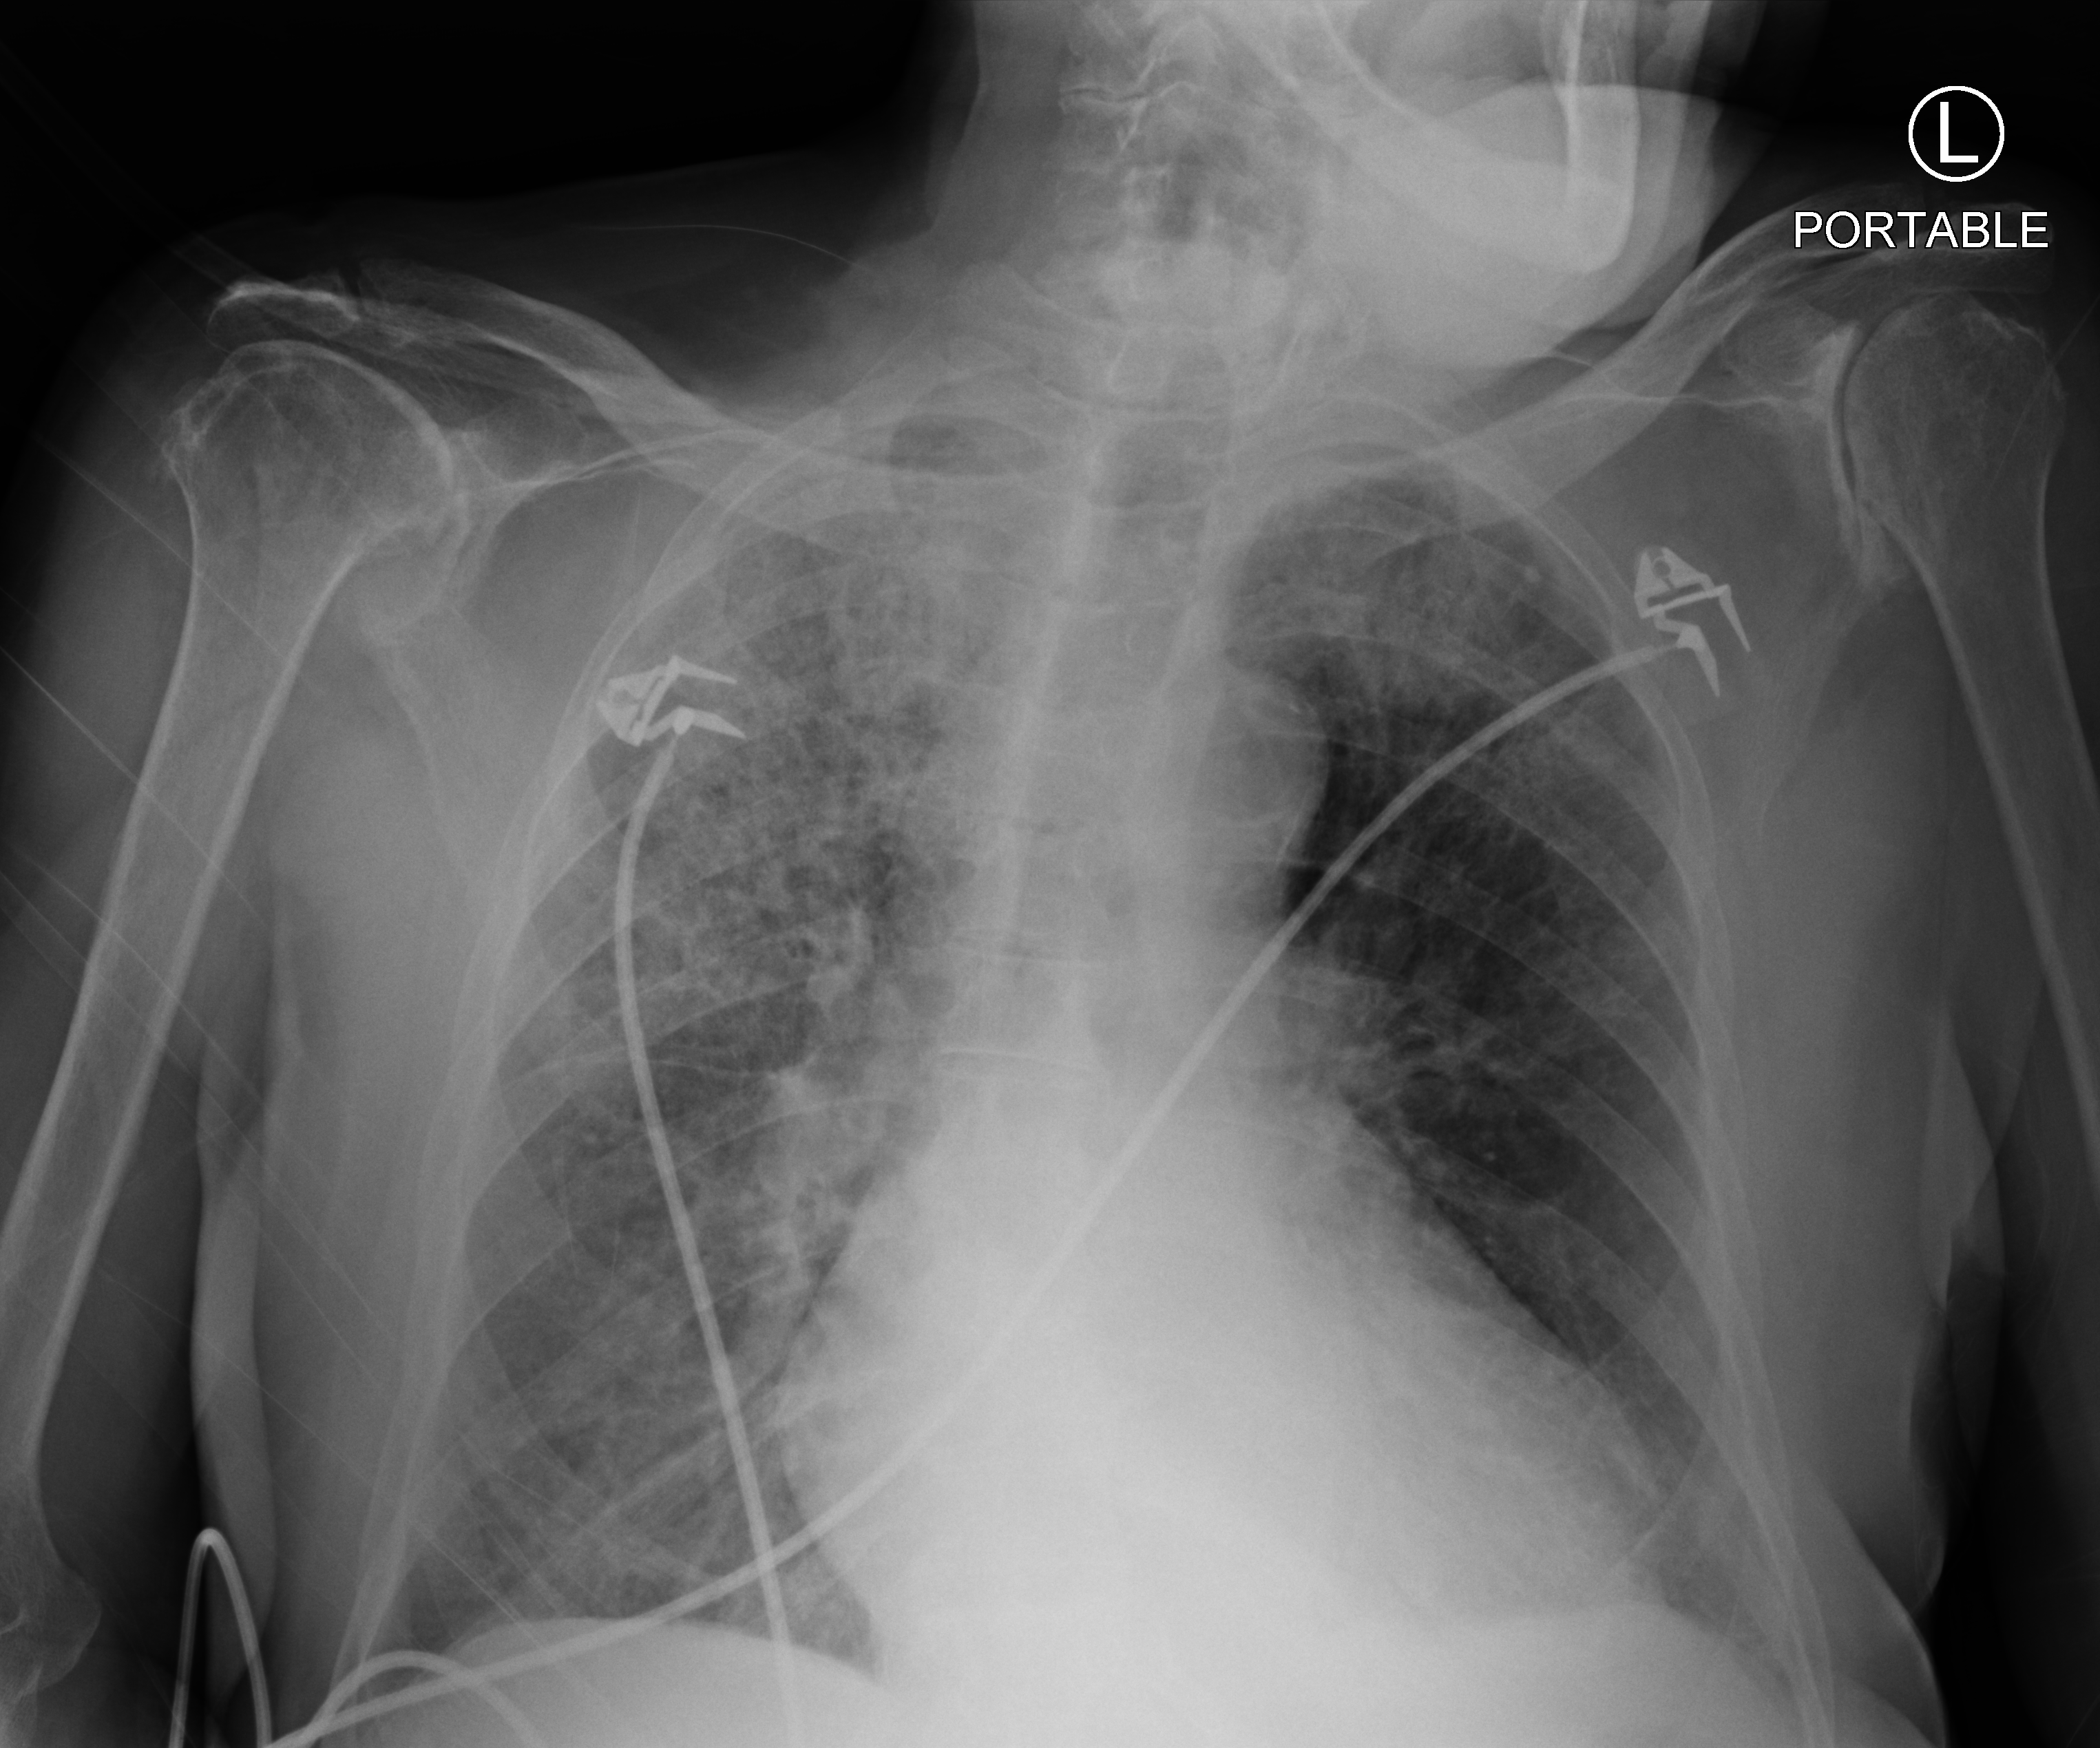
Bedside chest radiograph (computed radiography); anteroposterior (AP) projection. Patient hospitalised with COVID-19; male, aged 75–90 years.
Hospital-stay facts (about this admission, not read from this image; timing relative to this image not recorded): admitted to intensive care during this hospital stay: no.